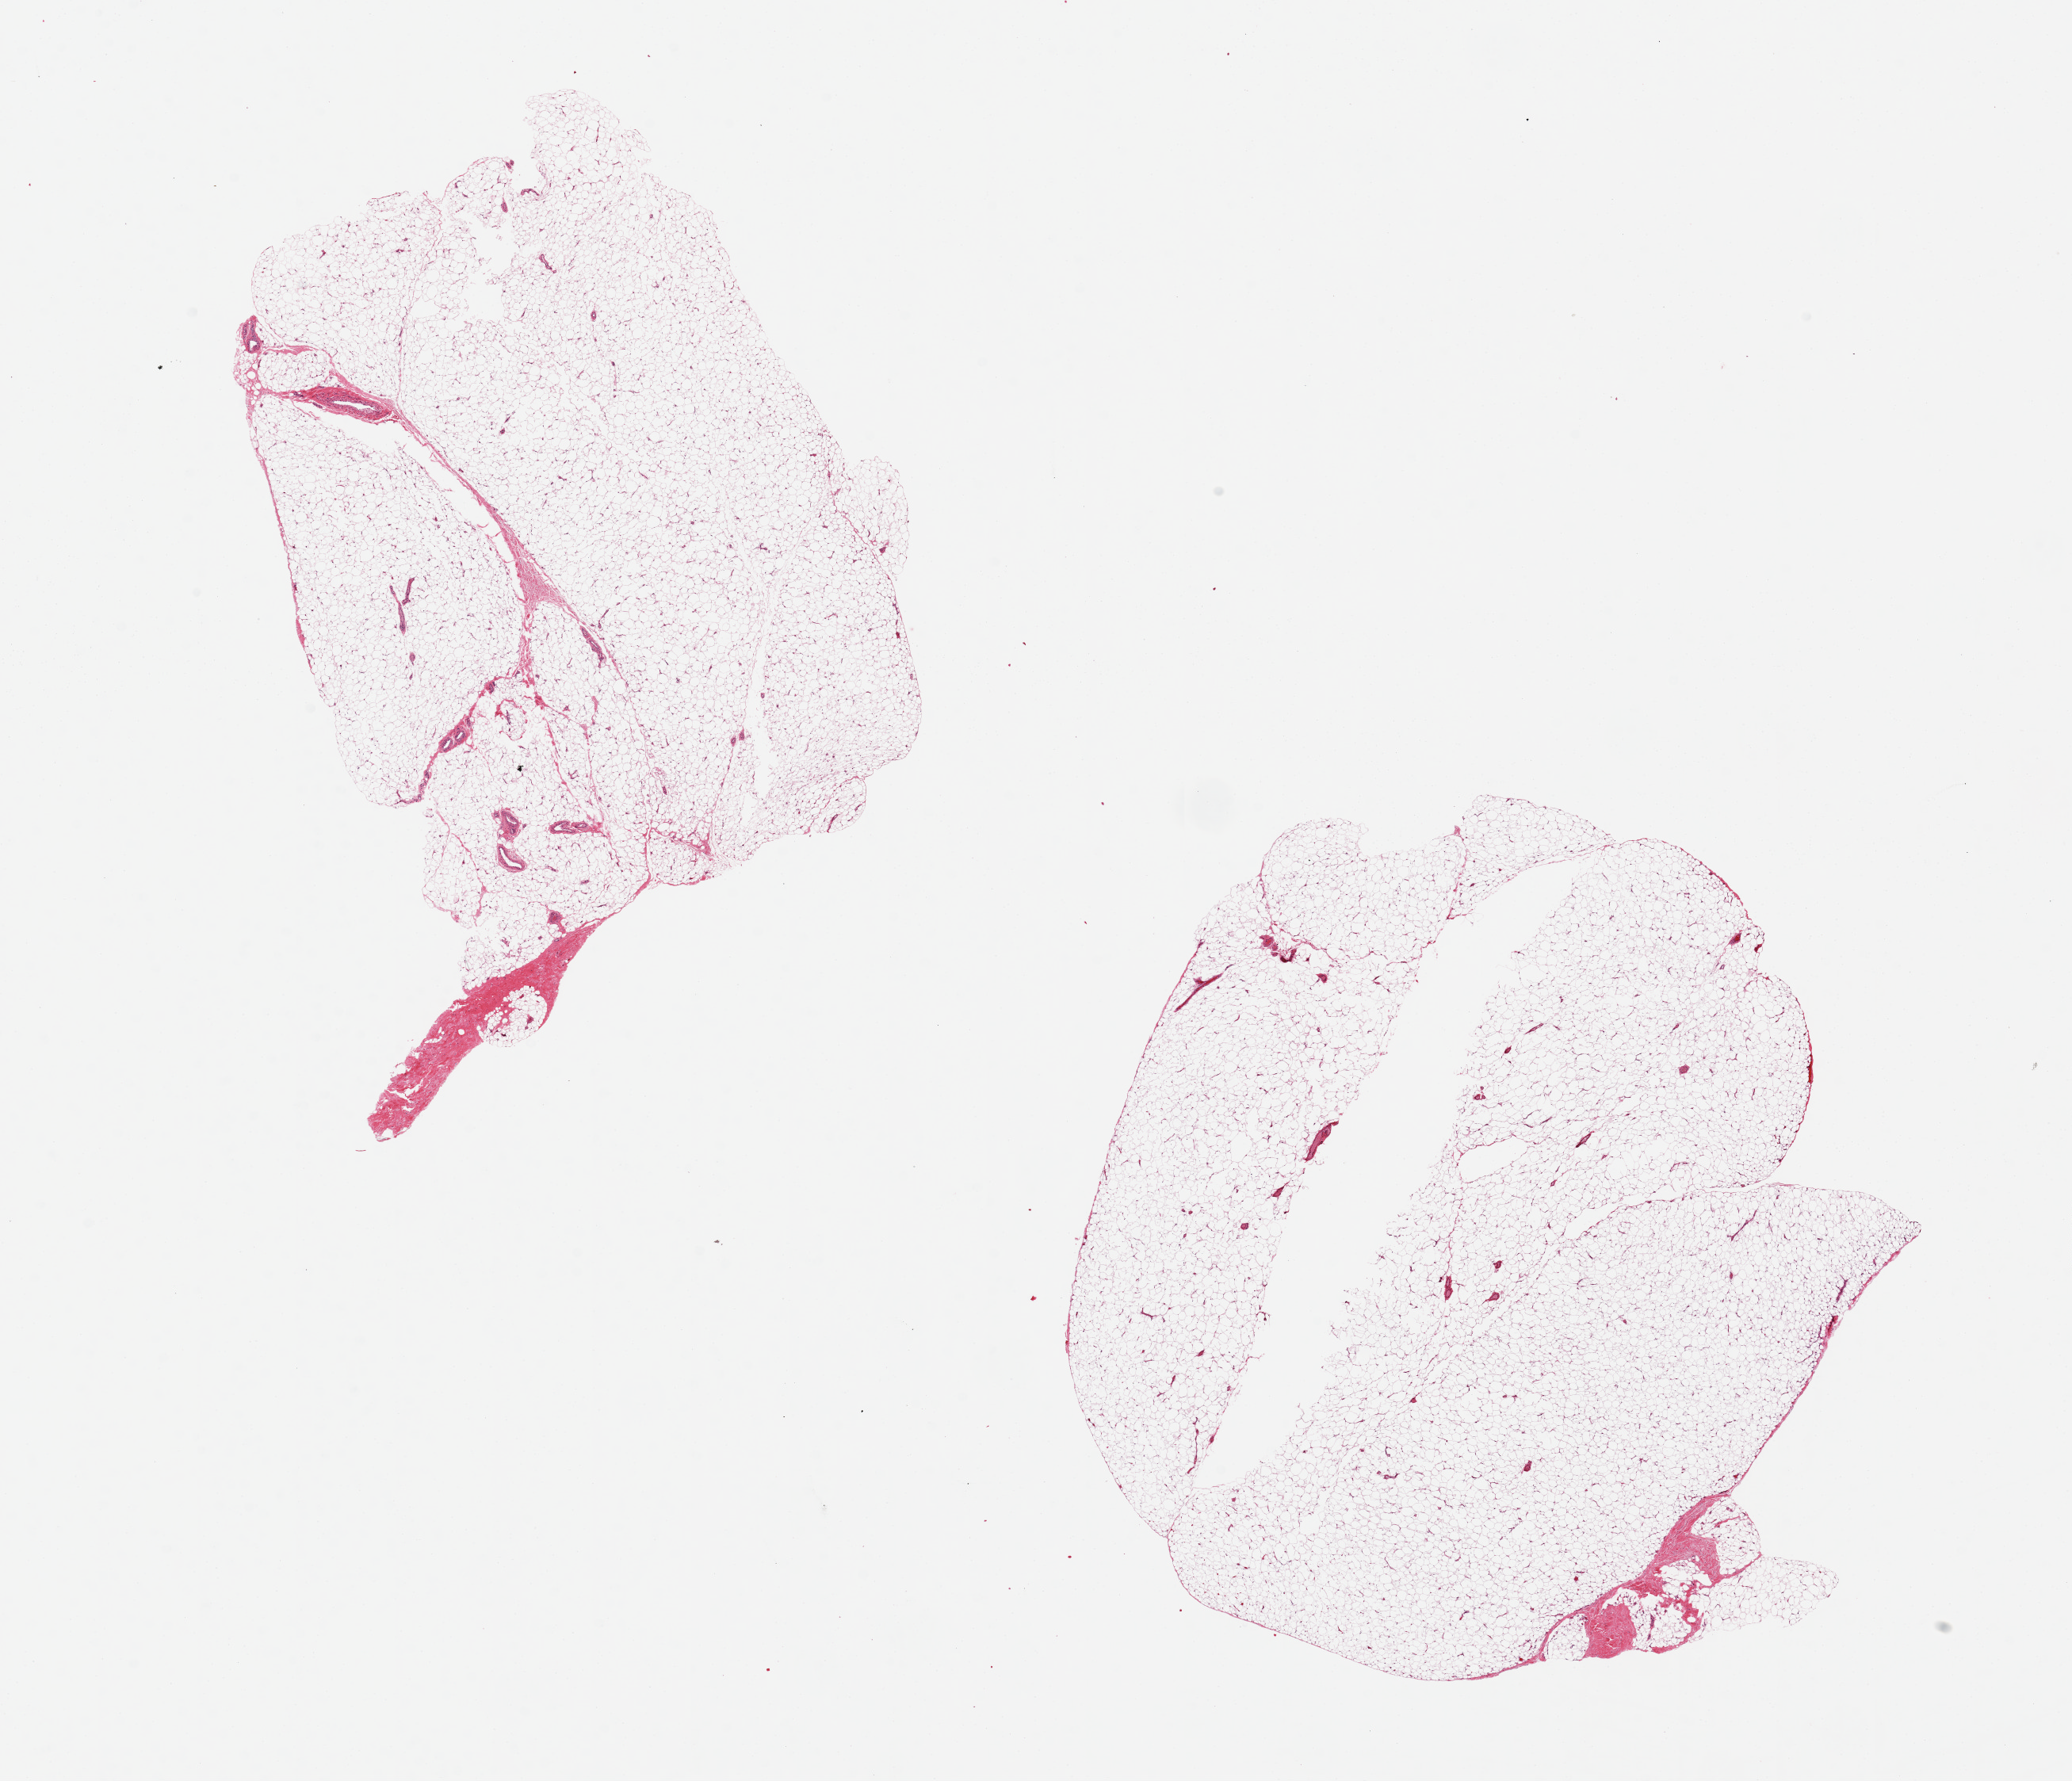
H&E whole-slide image, whole scanned area (about 20.7 x 17.8 mm) shown as a low-resolution overview, PAXgene-fixed, paraffin-embedded tissue, sampled site (target tissue): adipose tissue, tissue donor sample. Male donor.
- reviewer comment on this tissue sample: pieces 8x7 & 7x5 mm